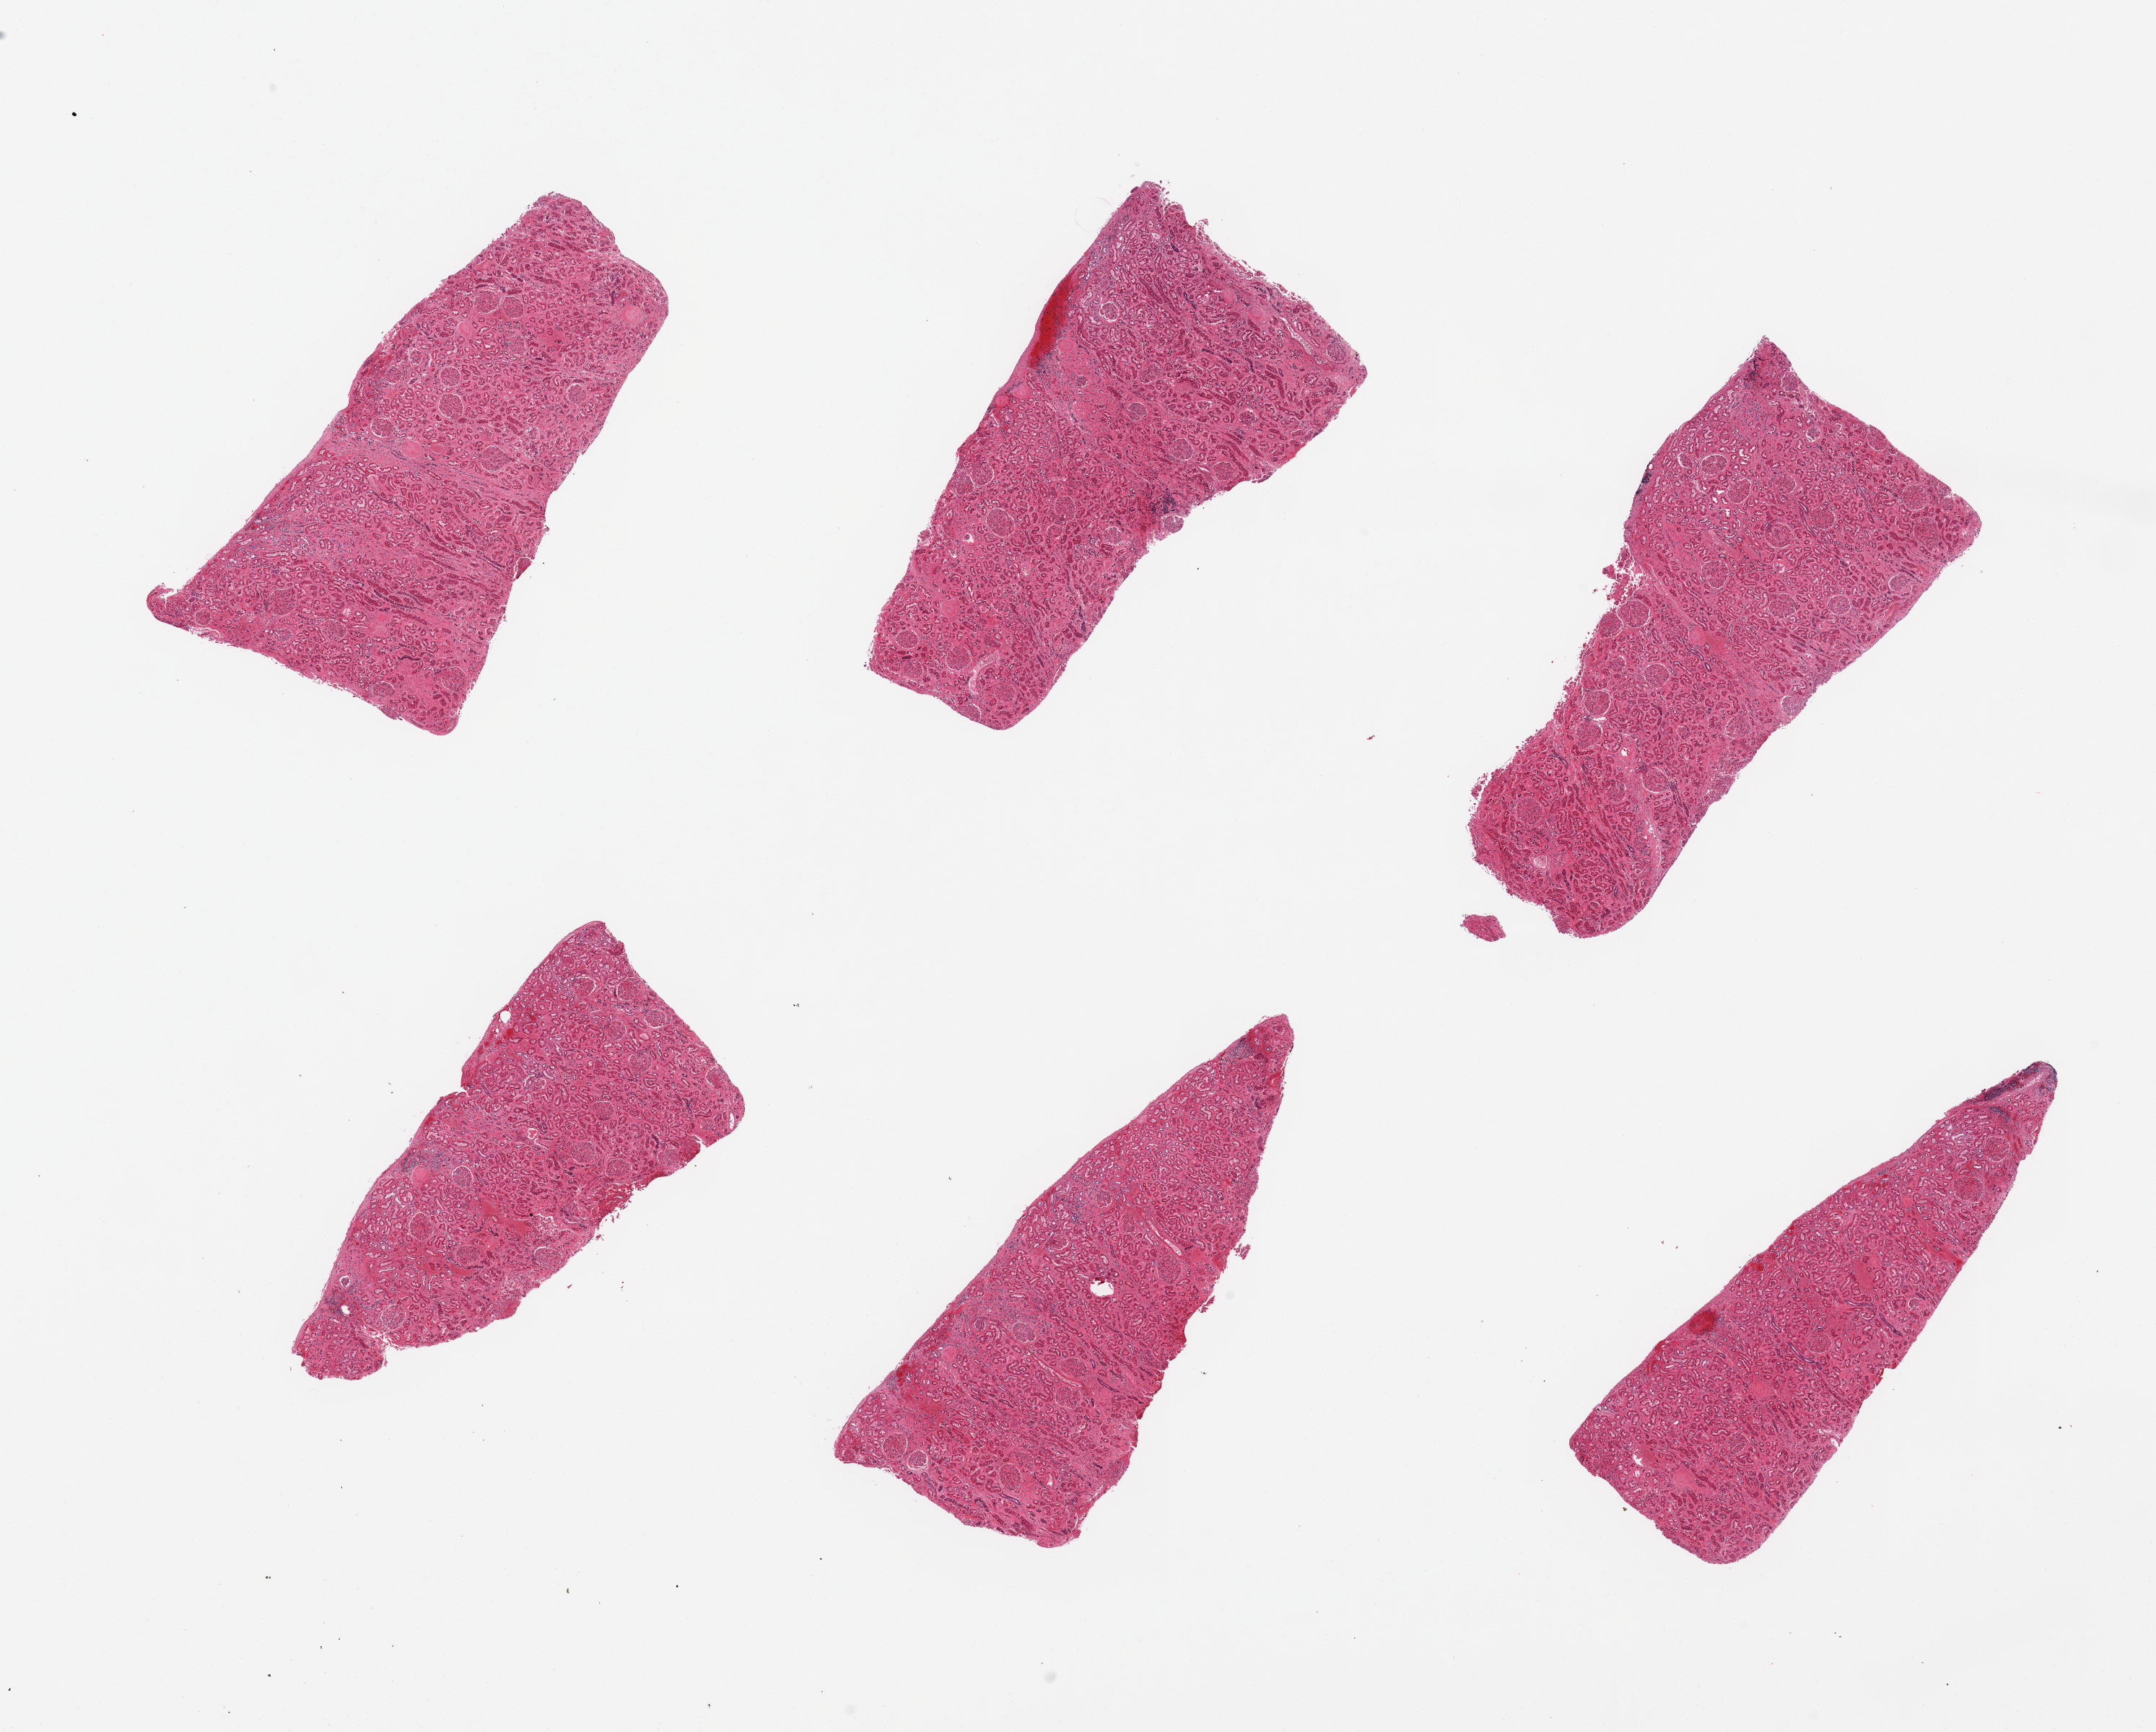
Digitized haematoxylin and eosin-stained section, brightfield — whole scanned area (about 23.6 x 19.0 mm, from a 20x scan) shown as a low-resolution overview, PAXgene-fixed paraffin-embedded (PFPE) section, section of renal cortex (target tissue), tissue donor sample. Male donor.
* review note (as recorded): 6 pieces; a few scattered sclerosed glomeruli; tubules moderately autolyzed